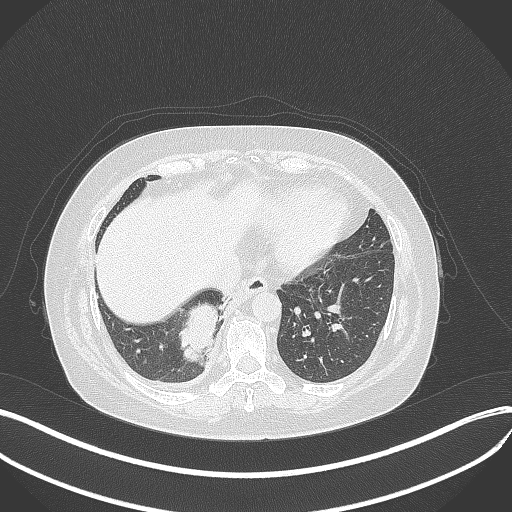
Chest CT, one axial slice. Slice 101 of 381 in the series (ordered by position). Reconstruction kernel B70f. 120 kVp. Lung window (W 1500 / L -600 HU). 512 × 512 image matrix. Female patient, age 56 years. From the clinical record (not read from this slice): clinical TNM (as recorded): T2b N1 M0; histopathological grade: G3.
Outlined on this slice (bounding box drawn by a radiologist):
- lung tumour (recorded histology: small cell carcinoma): bounding box (x1, y1, x2, y2) in pixels: (175, 298, 221, 367)